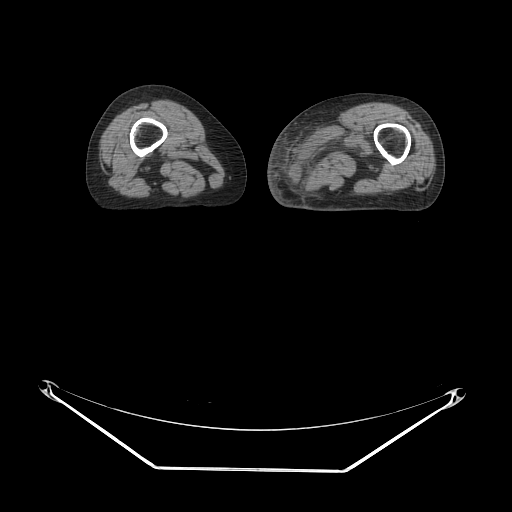
CT of an extremity soft-tissue mass (from a PET/CT study), one axial slice; position 12 of 91 along the scan axis; 140 kVp; soft-tissue window (W 400 / L 40 HU); 512 × 512 image matrix. Female patient. Case-level facts recorded for this patient, not image findings: histological type: pleomorphic leiomyosarcoma; grade: high; site of the primary tumour: left thigh.
Structures marked on this image (expert contour drawn on MRI and transferred to this co-registered scan by the dataset authors):
- gross tumour volume including surrounding oedema: bounding box [x1, y1, x2, y2] px = [295, 116, 380, 188]